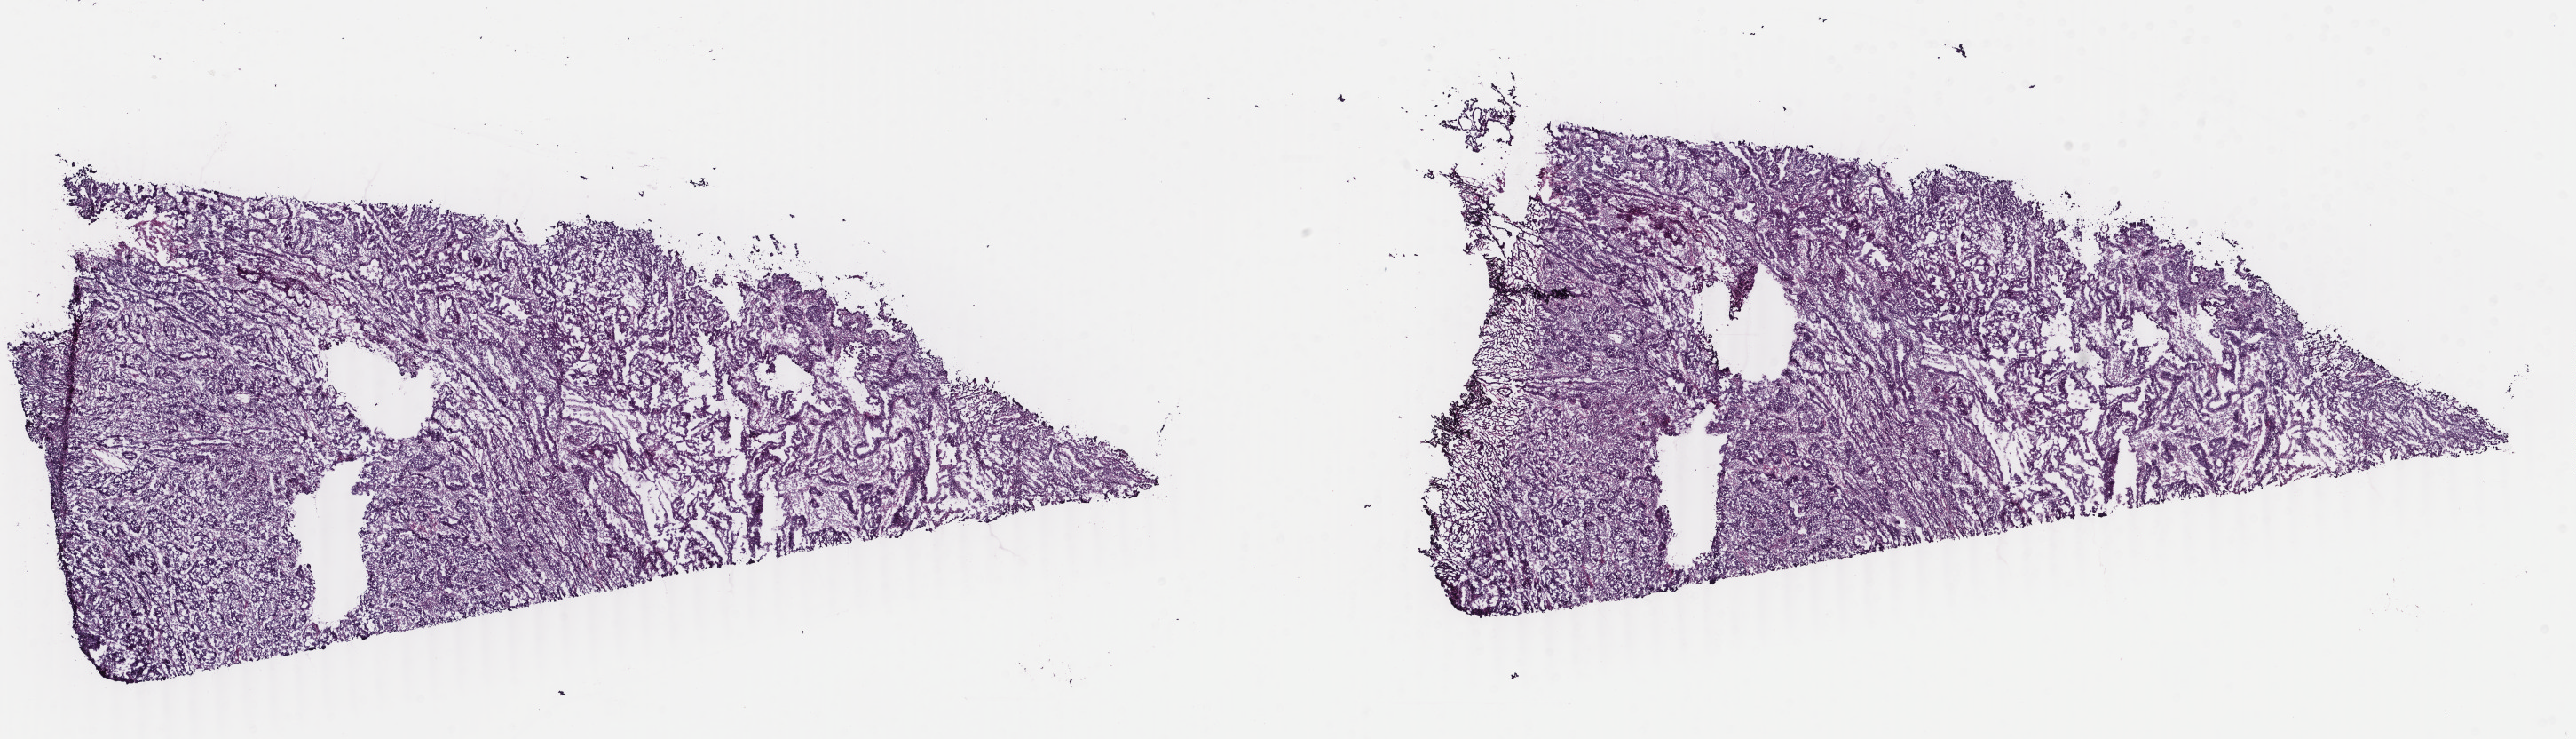
Digitized H&E tissue section (whole slide), shown as a low-resolution overview of the whole scanned area (about 23.1 x 6.6 mm, slide scanned at 40x). Frozen section from the top of the tissue portion. Primary tumour sample from the uterus. Patient: female, age at initial diagnosis 65 years. Histologic grade: G3 (poorly differentiated). Composition of this section per pathologist review: tumour cells 90%, tumour nuclei 90%, normal cells 0%, stromal cells 3%, necrosis 7%. Inflammatory infiltration, as recorded: lymphocyte infiltration 30%, monocyte infiltration 25%, neutrophil infiltration 2%.
Histologic diagnosis: Adenocarcinoma, NOS (endometrium). FIGO stage: IVB. Lymph nodes positive (case pathology): 0 of 7 examined.